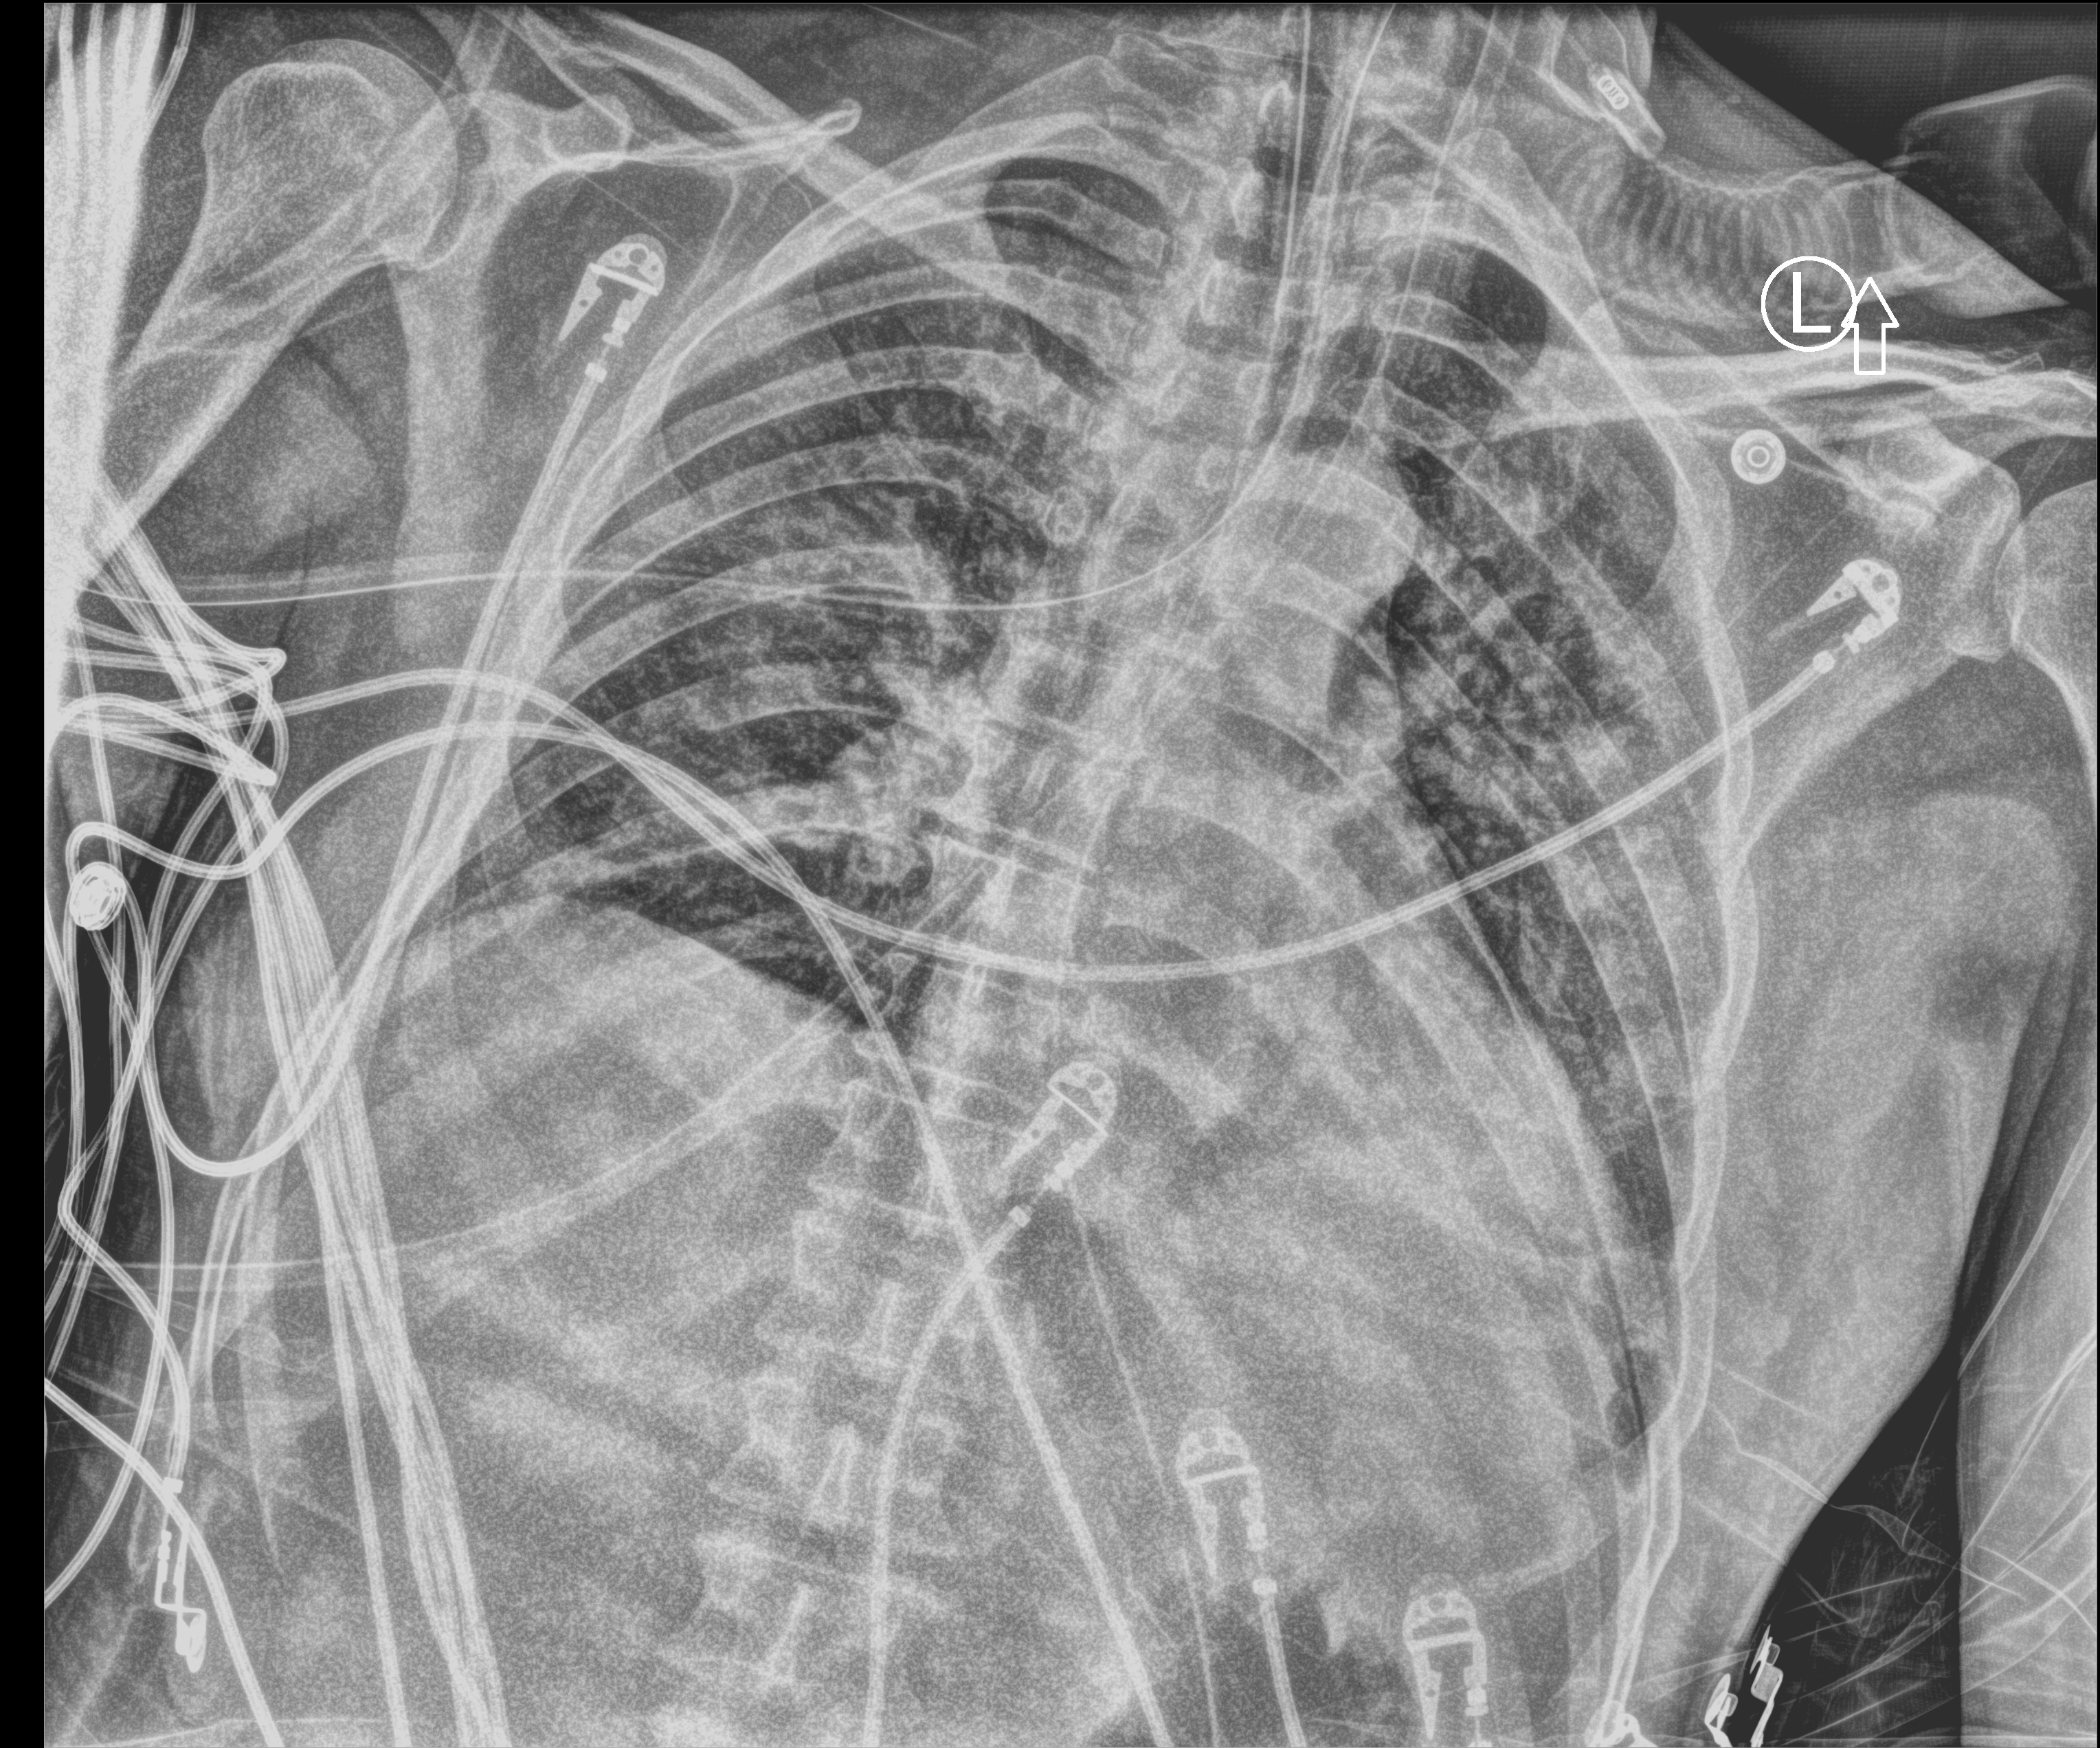
Portable chest radiograph. Patient hospitalised with COVID-19; male, aged 18–59 years.
Hospital-stay facts (about this admission, not read from this image; timing relative to this image not recorded):
- chronic kidney disease (admission record): no
- length of hospital stay: 14 days